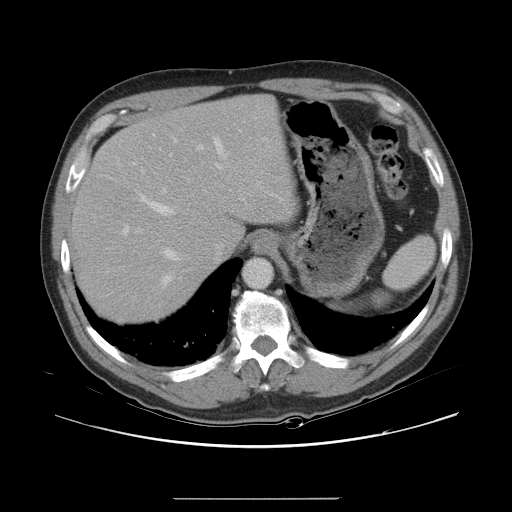
Contrast-enhanced abdominal CT, one axial slice; slice 23 of 40 in the series (ordered by position); intravenous contrast given; soft-tissue window (W 400 / L 40 HU); 5 mm slice thickness; 512 × 512 image matrix, field of view 408 × 408 mm. Male patient, age 64 years. From the clinical record (not read from this slice): diagnosis: colorectal cancer liver metastases, imaged before liver resection; multiple liver metastases: yes; largest metastasis: 3.2 cm; disease in both lobes: yes.
Structures marked on this image (outlined manually by an expert reader):
- hepatic veins: bounding box [x1, y1, x2, y2] px = [139, 134, 265, 285]
- liver: [74, 95, 293, 321]
- planned liver remnant (the part of the liver to remain after resection): [74, 95, 293, 268]
- portal vein (with intrahepatic branches): [122, 144, 205, 236]